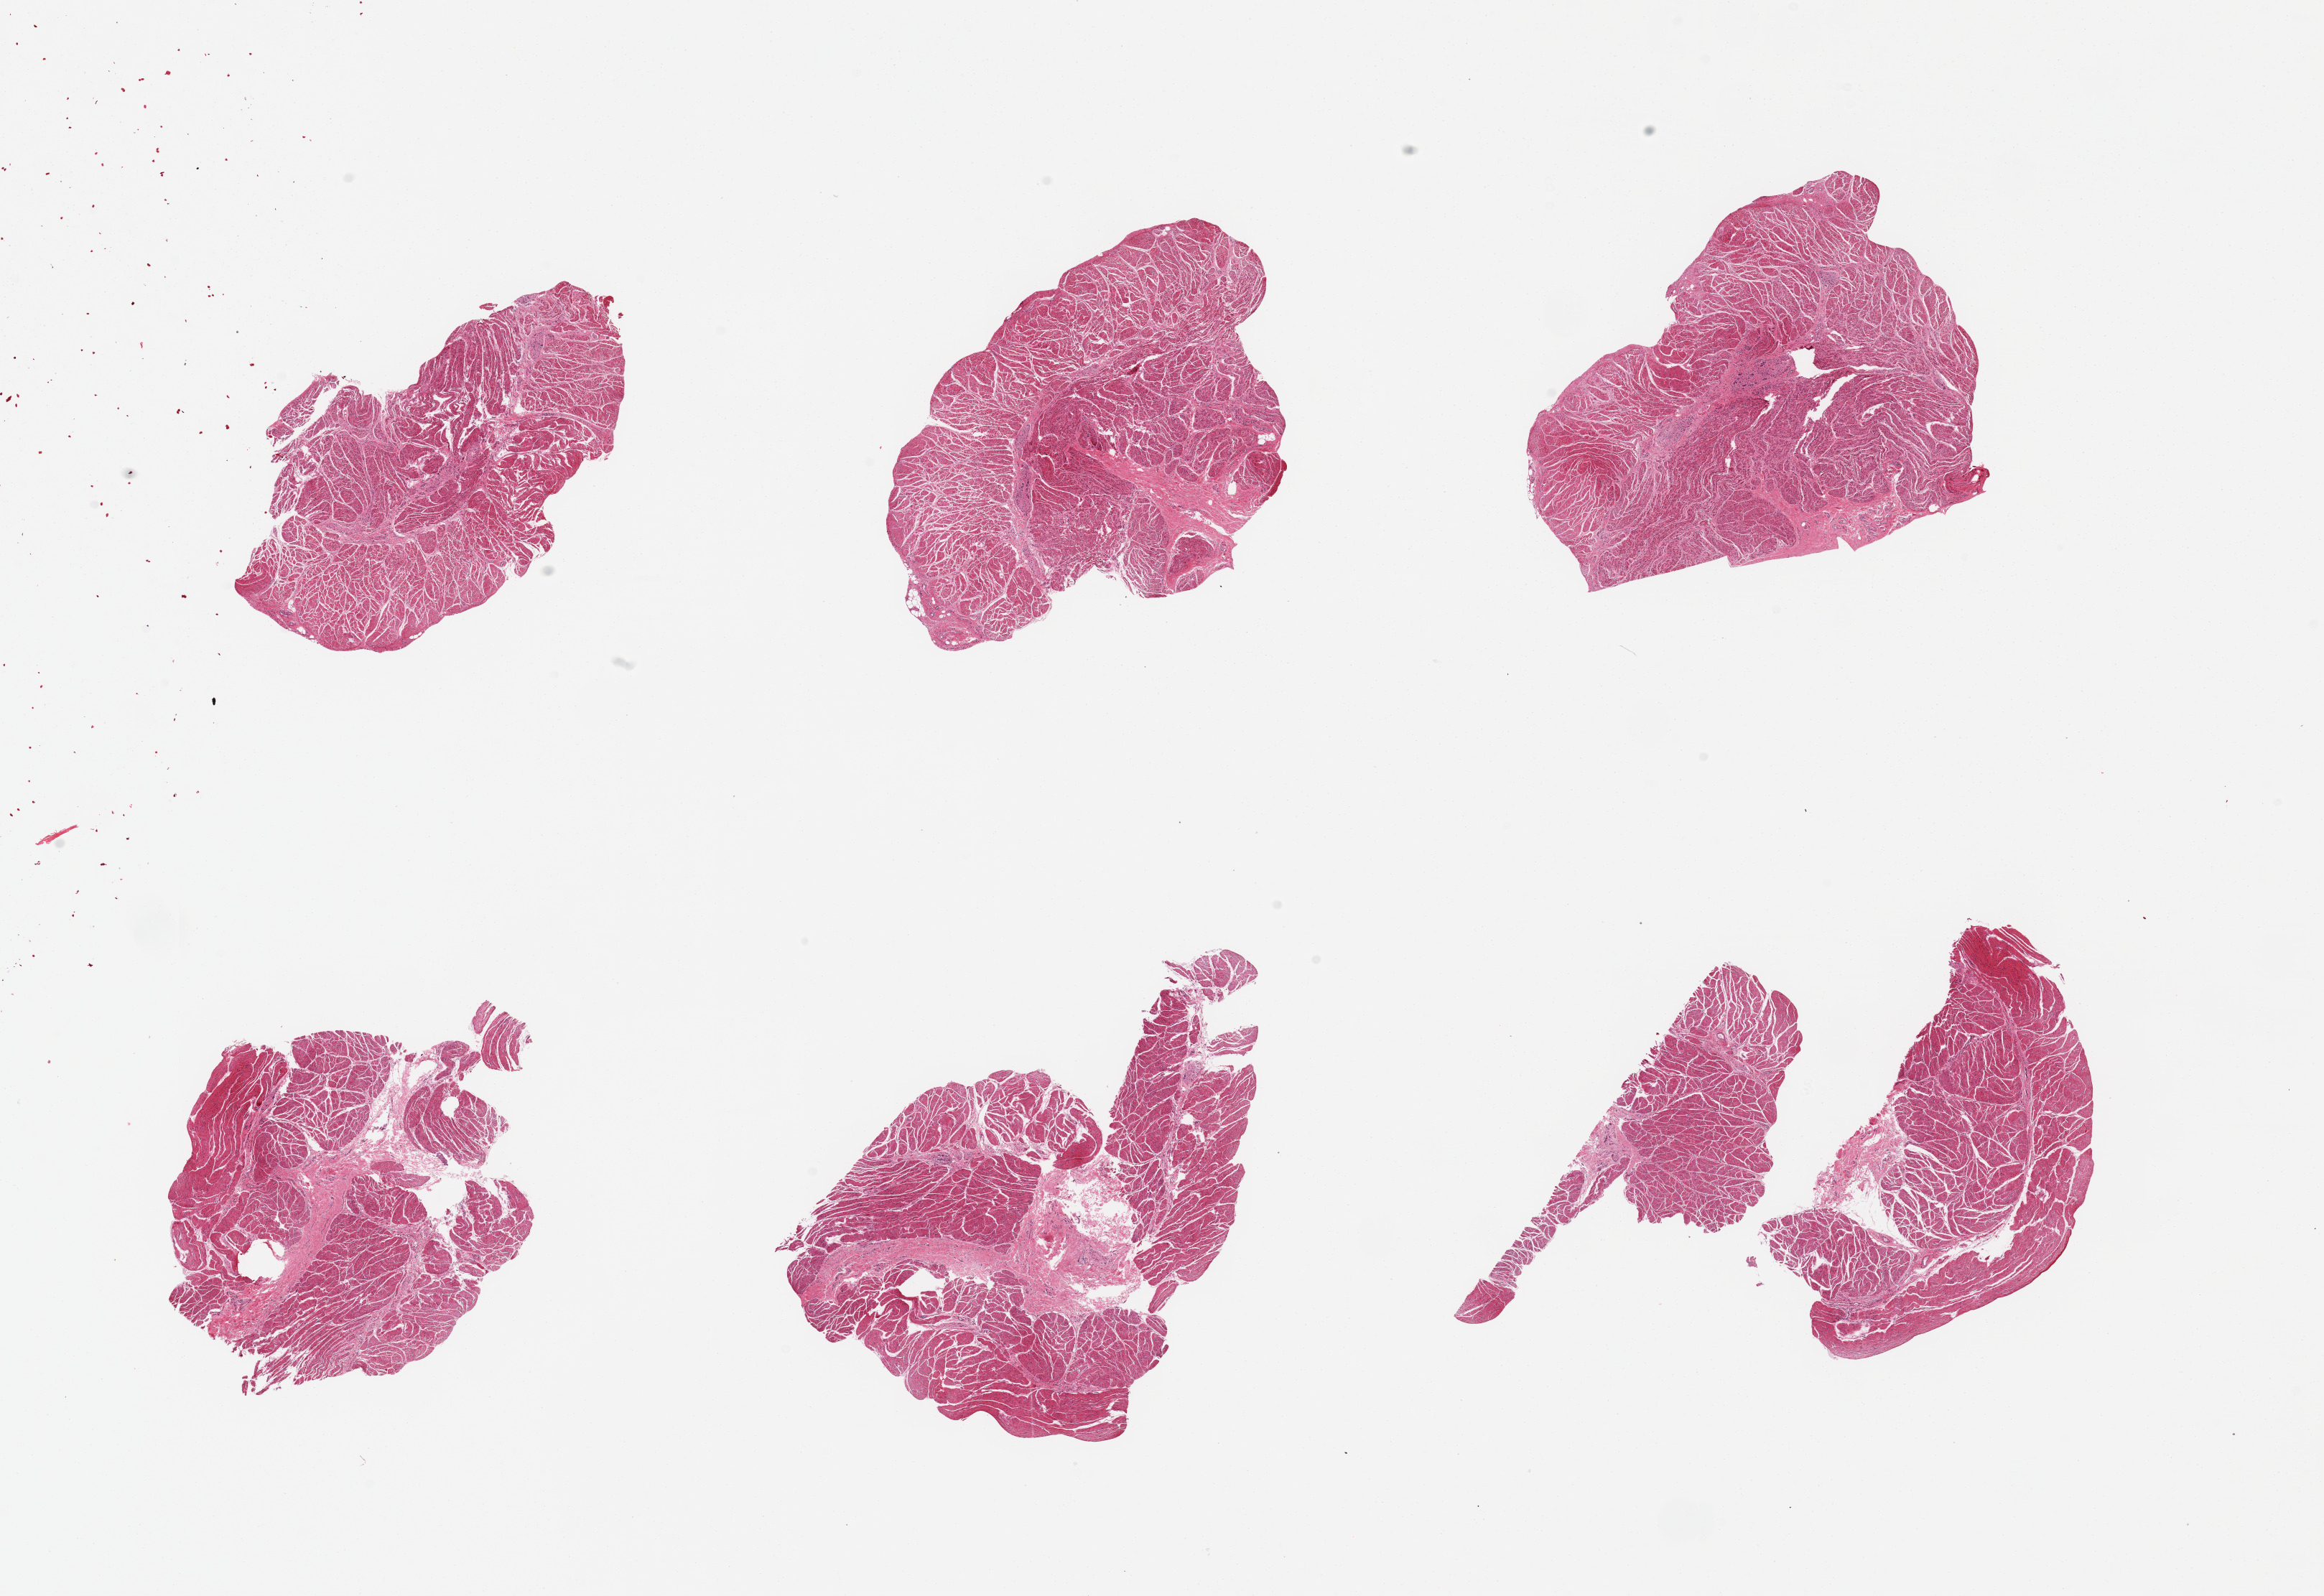
Digitized hematoxylin and eosin (H&E)-stained section, shown as a low-resolution overview of the whole scanned area (about 25.6 x 17.6 mm), PAXgene-fixed, paraffin-embedded tissue, section of esophageal muscle (target tissue), tissue donor sample. Male donor.
Review note (as recorded): 2 pieces, confirmed target muscularis.